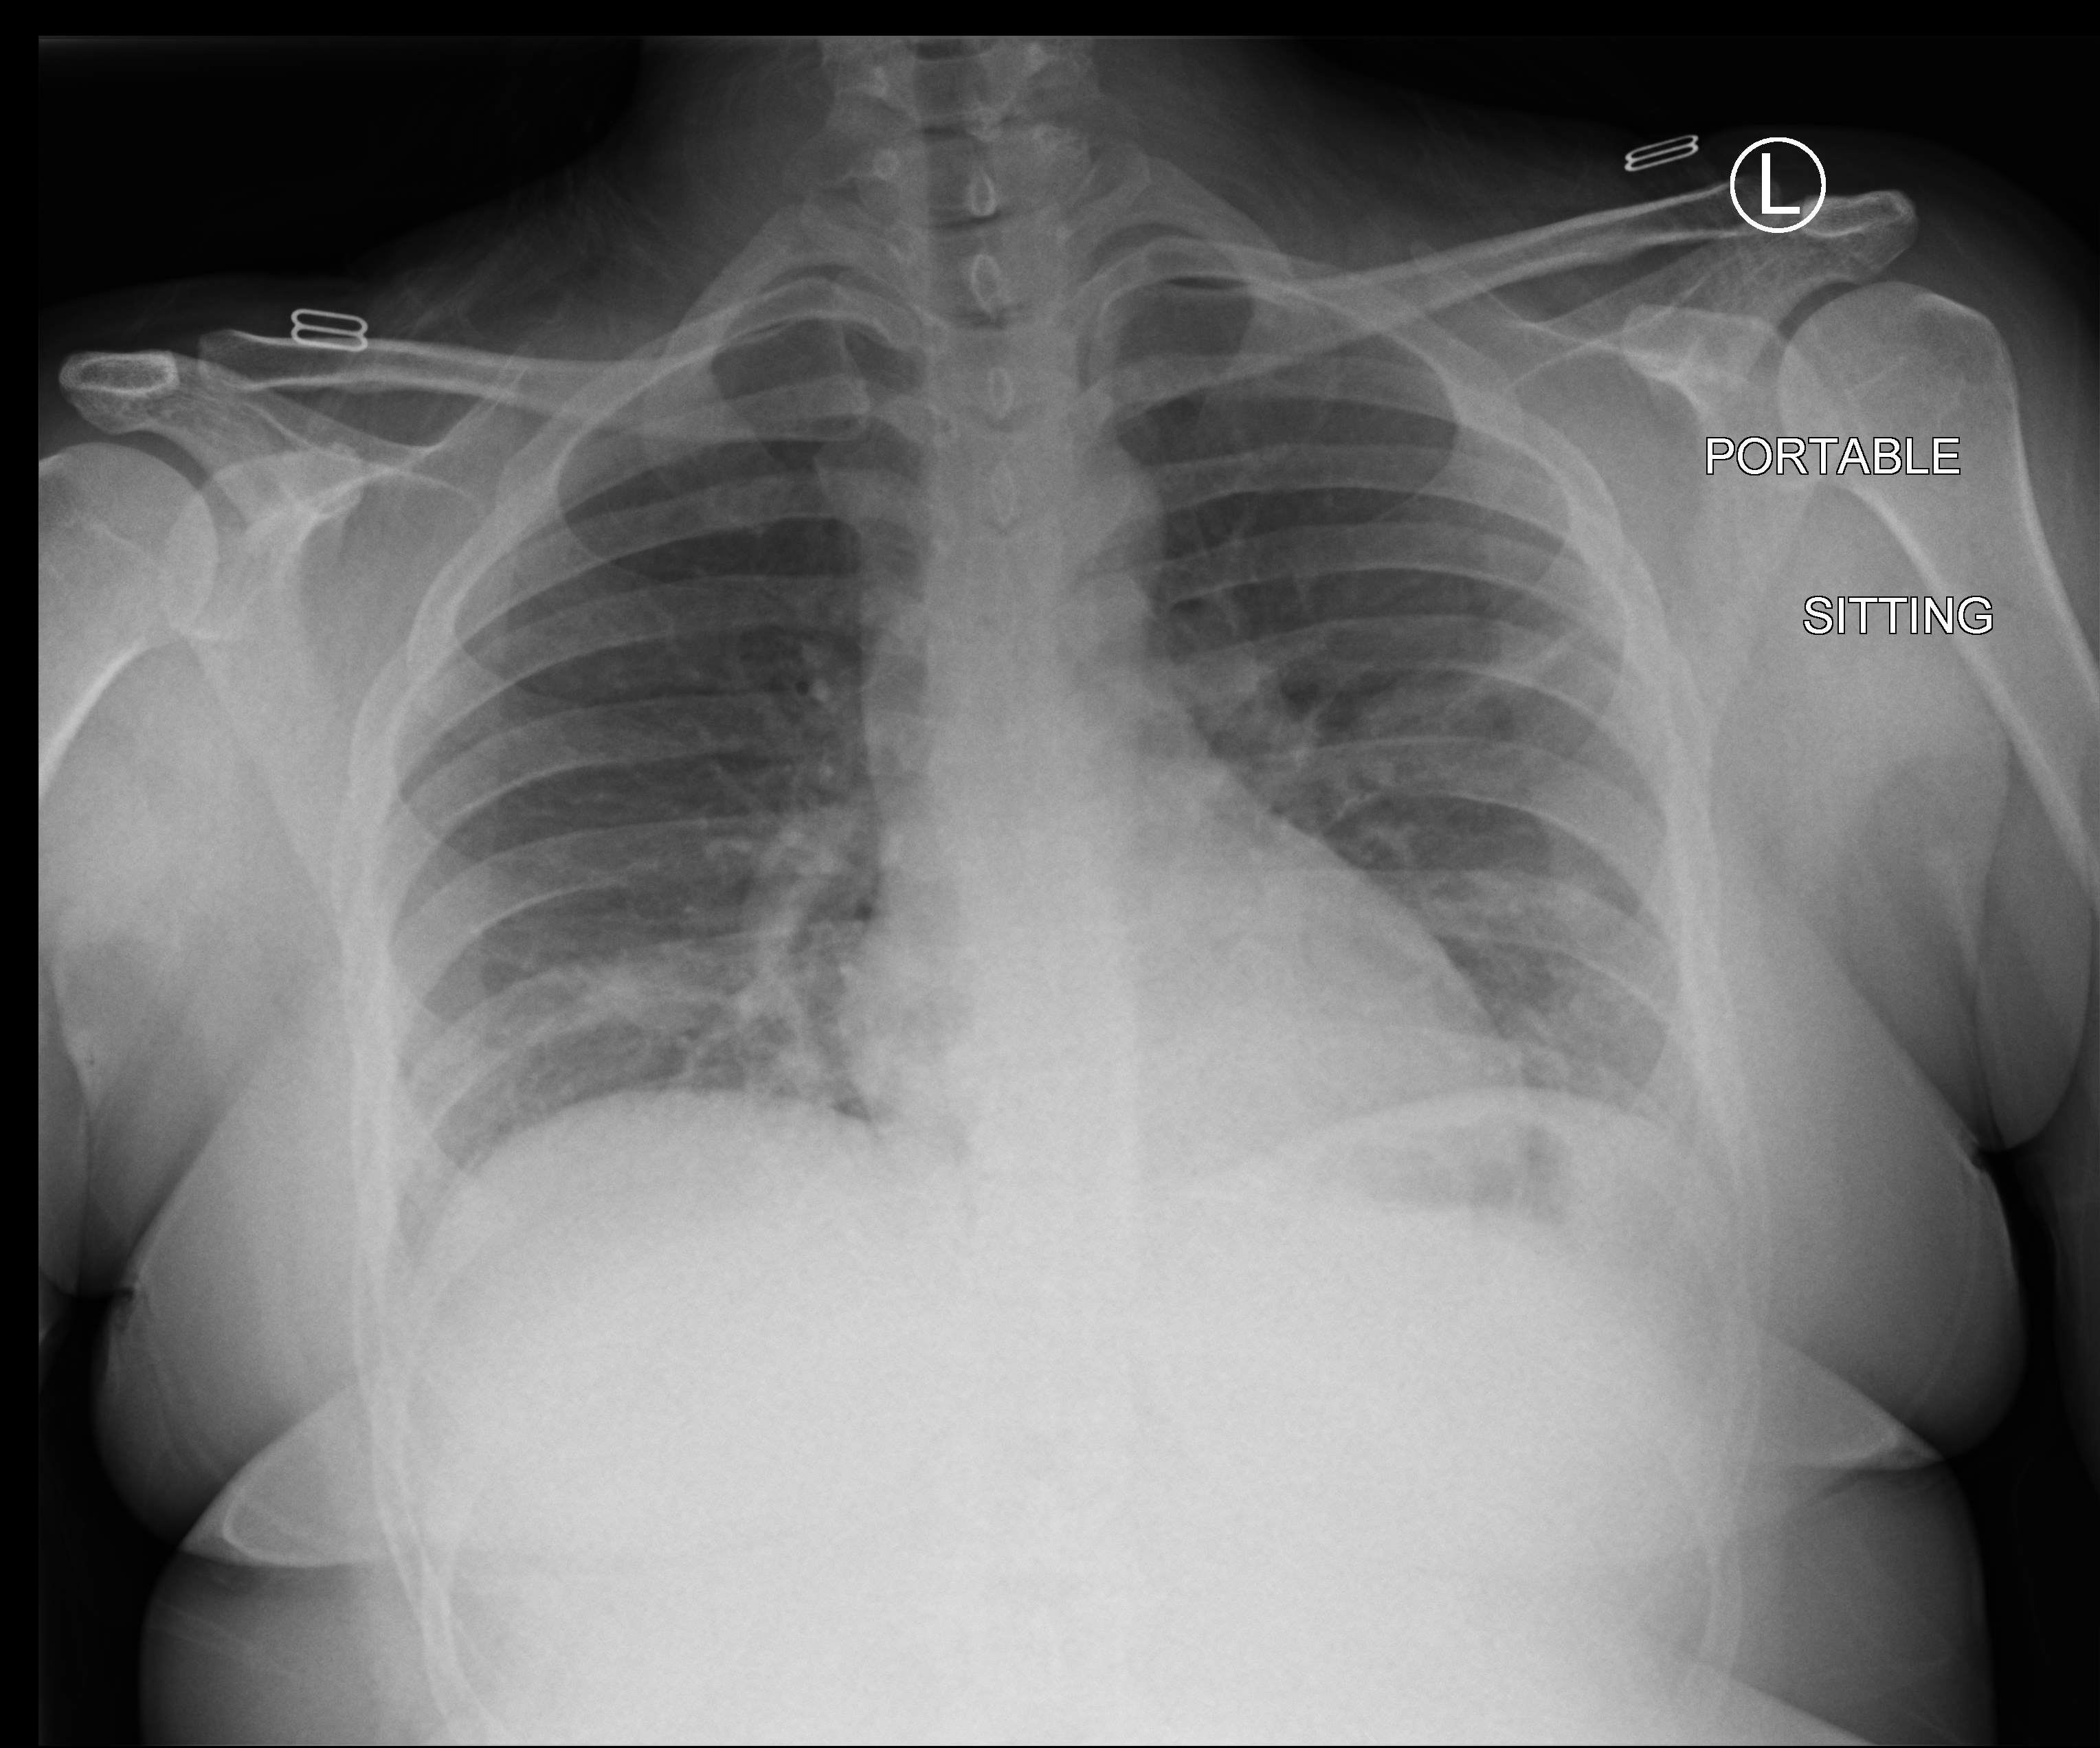
Portable chest radiograph, anteroposterior (AP) projection. Female patient hospitalised with COVID-19, age 18–59 years.
Admission-level facts for this patient (not findings on this image; timing relative to this image not recorded):
- COPD (admission record): no
- length of hospital stay: 1 day
- admitted to intensive care during this hospital stay: no